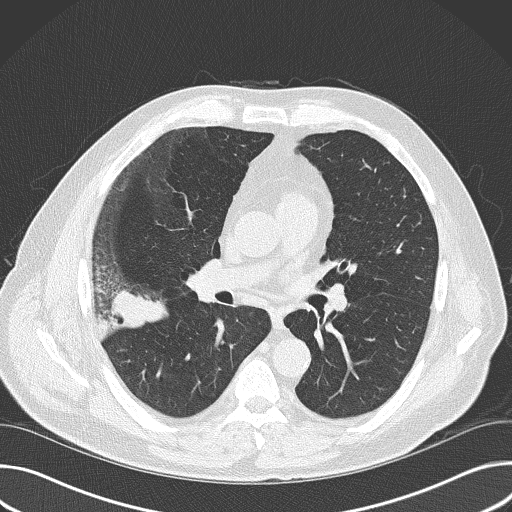
Low-dose screening chest CT, axial slice, baseline screening round, lung window (W 1500 / L -600 HU), 2 mm slice thickness, 120 kVp, slice 91 of 157 in the series. Male participant, aged 56 years at enrolment.
Expert reader's lesion annotation, bounding box [x1, y1, x2, y2] px = [79, 254, 182, 355]. Reader record for this screening exam (exam-level; its link to the box is not recorded): non-calcified nodule or mass ≥4 mm, right upper lobe, 6 × 5 mm, spiculated (stellate) margins, soft tissue attenuation. Official screen result: positive, change unspecified: nodule(s) >= 4 mm or enlarging nodule(s), mass(es), or other non-specific abnormalities suspicious for lung cancer. Later outcome: lung cancer diagnosed 16 days after this screen — adenocarcinoma, NOS, right upper lobe, poorly differentiated (G3), stage IIB (AJCC 6th edition), 60 mm at pathology.